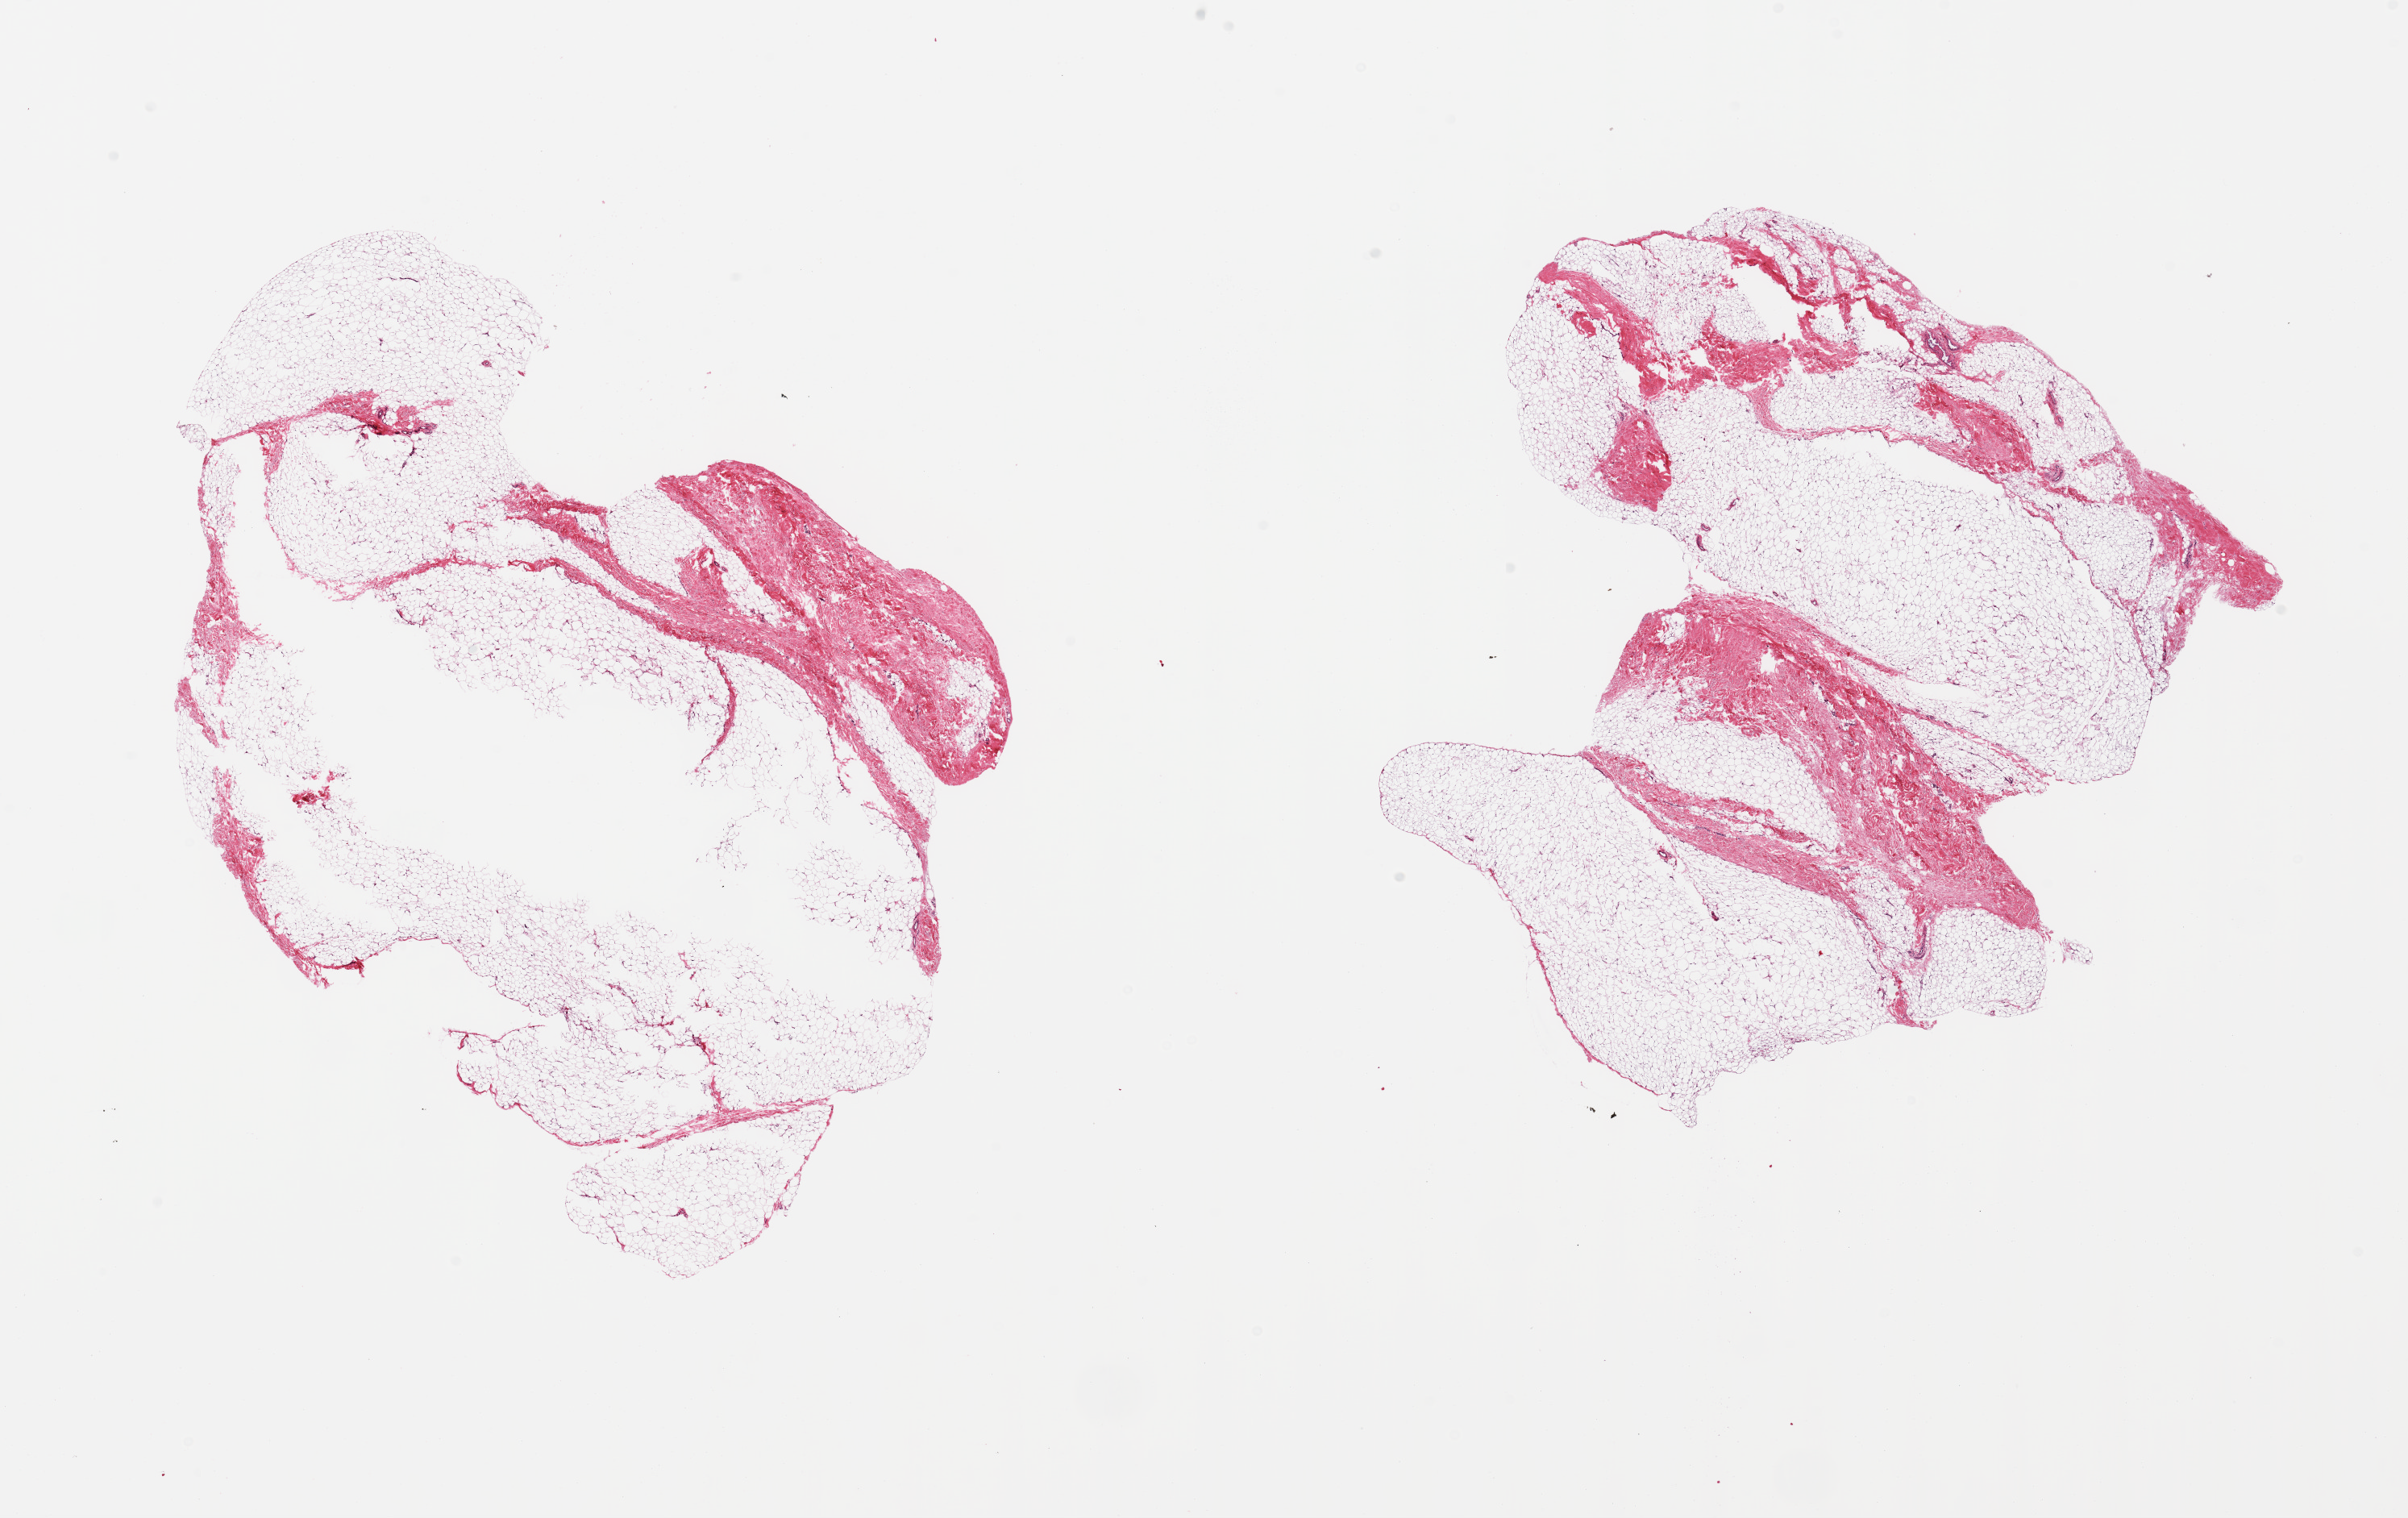
Whole-slide image, haematoxylin and eosin stain — whole scanned area (about 23.6 x 14.9 mm) shown as a low-resolution overview, PAXgene-fixed, paraffin-embedded tissue, section of breast (target tissue), tissue donor sample. Male donor.
Reviewer comment on this tissue sample: 2 pieces, fibroadipose elements only.